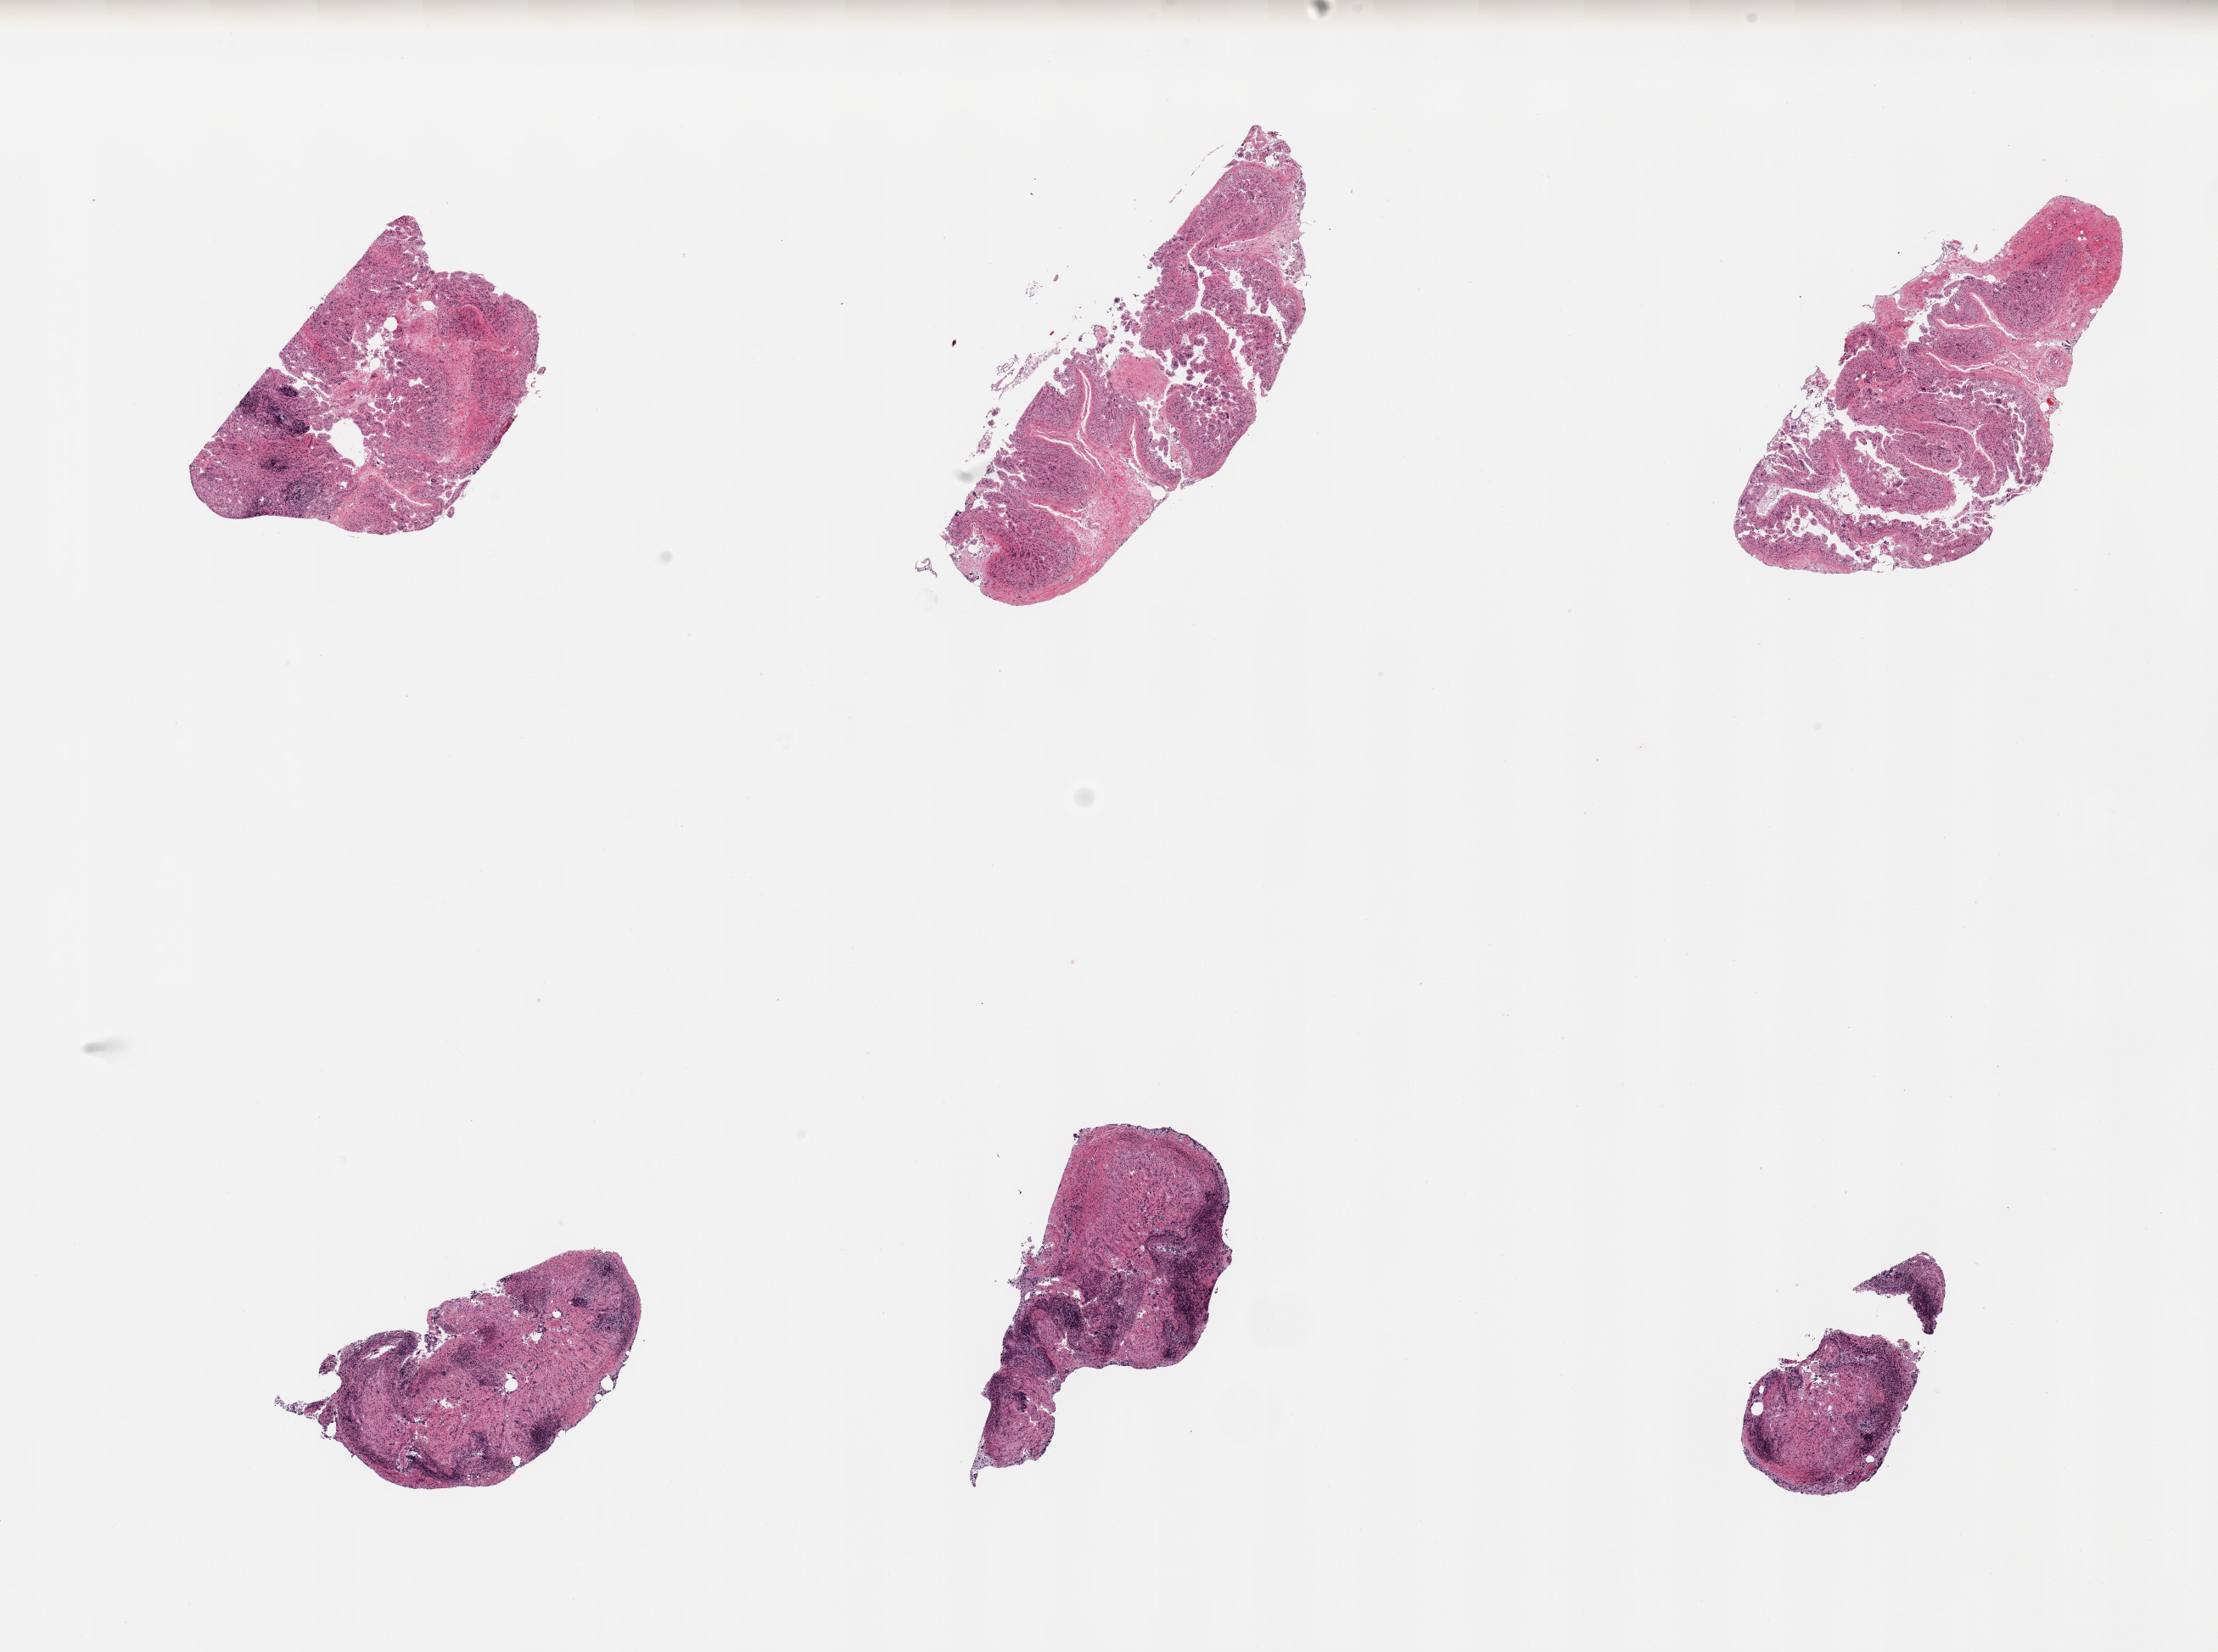
Whole-slide image, haematoxylin and eosin stain — low-resolution overview of the scanned area, about 20.7 x 15.4 mm; PAXgene-fixed, paraffin-embedded tissue; section of ileum (target tissue); donor tissue sample. Donor sex: female.
Pathologist's review note for this sample: 6 pieces; autolyzed mucosa with target lymphoid tissue in 4 pieces.